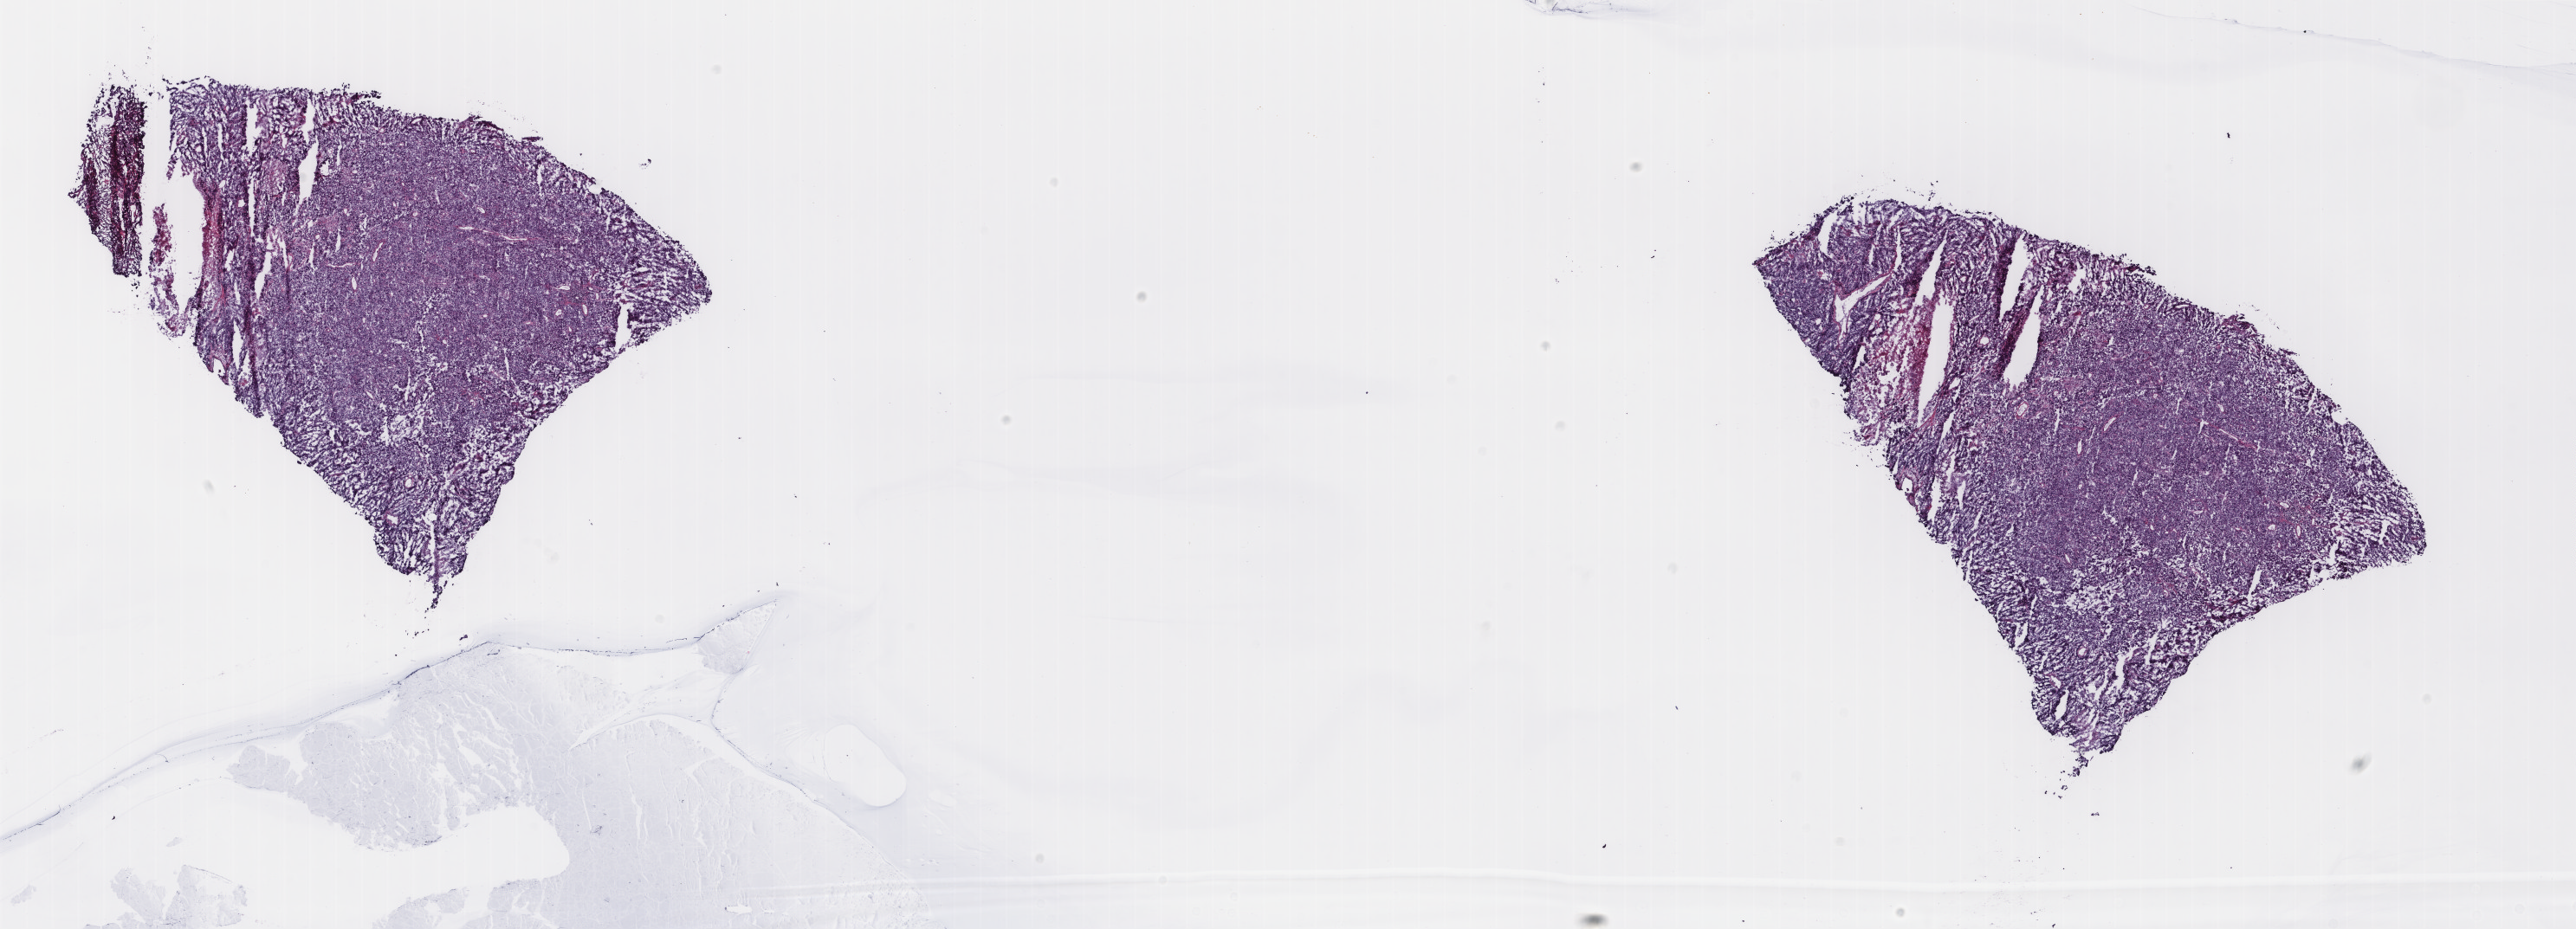
Digitized Hematoxylin and eosin (H&E) stained tissue section (whole slide) — whole scanned area (about 23.6 x 8.5 mm, slide scanned at 40x) shown as a low-resolution overview. Frozen section. Sample: primary tumour, uterus. Female patient; age at initial diagnosis 67 years. Histologic grade: G3 (poorly differentiated). Composition of this section per pathologist review: tumour cells 80%, tumour nuclei 80%, normal cells 0%, stromal cells 5%, necrosis 15%. Infiltration values recorded for this section: lymphocyte infiltration 20%, monocyte infiltration 20%, neutrophil infiltration 40%.
- histologic diagnosis: Endometrioid adenocarcinoma, NOS (endometrium)
- FIGO stage: IA